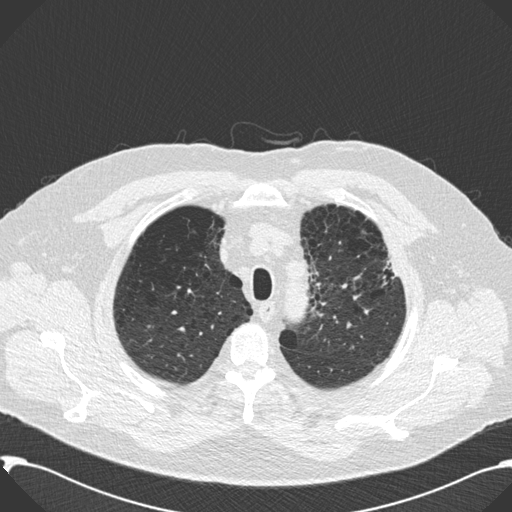
Low-dose screening chest CT, axial slice. Second annual screen. Lung window (W 1500 / L -600 HU). 120 kVp. Male, age 59 years at enrolment. Current smoker at enrolment.
• Expert-annotated lung lesion, bounding box [x1, y1, x2, y2] px = [367, 246, 409, 306].
• Screening reader's record for this exam: no non-calcified nodule ≥4 mm recorded.
• Official screen result: negative screen, significant abnormalities not suspicious for lung cancer.
• Later outcome: lung cancer diagnosed 518 days after this screen (after the third annual screen) — bronchiolo-alveolar carcinoma, mixed mucinous and non-mucinous, left upper lobe, stage IA (AJCC 6th edition), 20 mm at pathology.